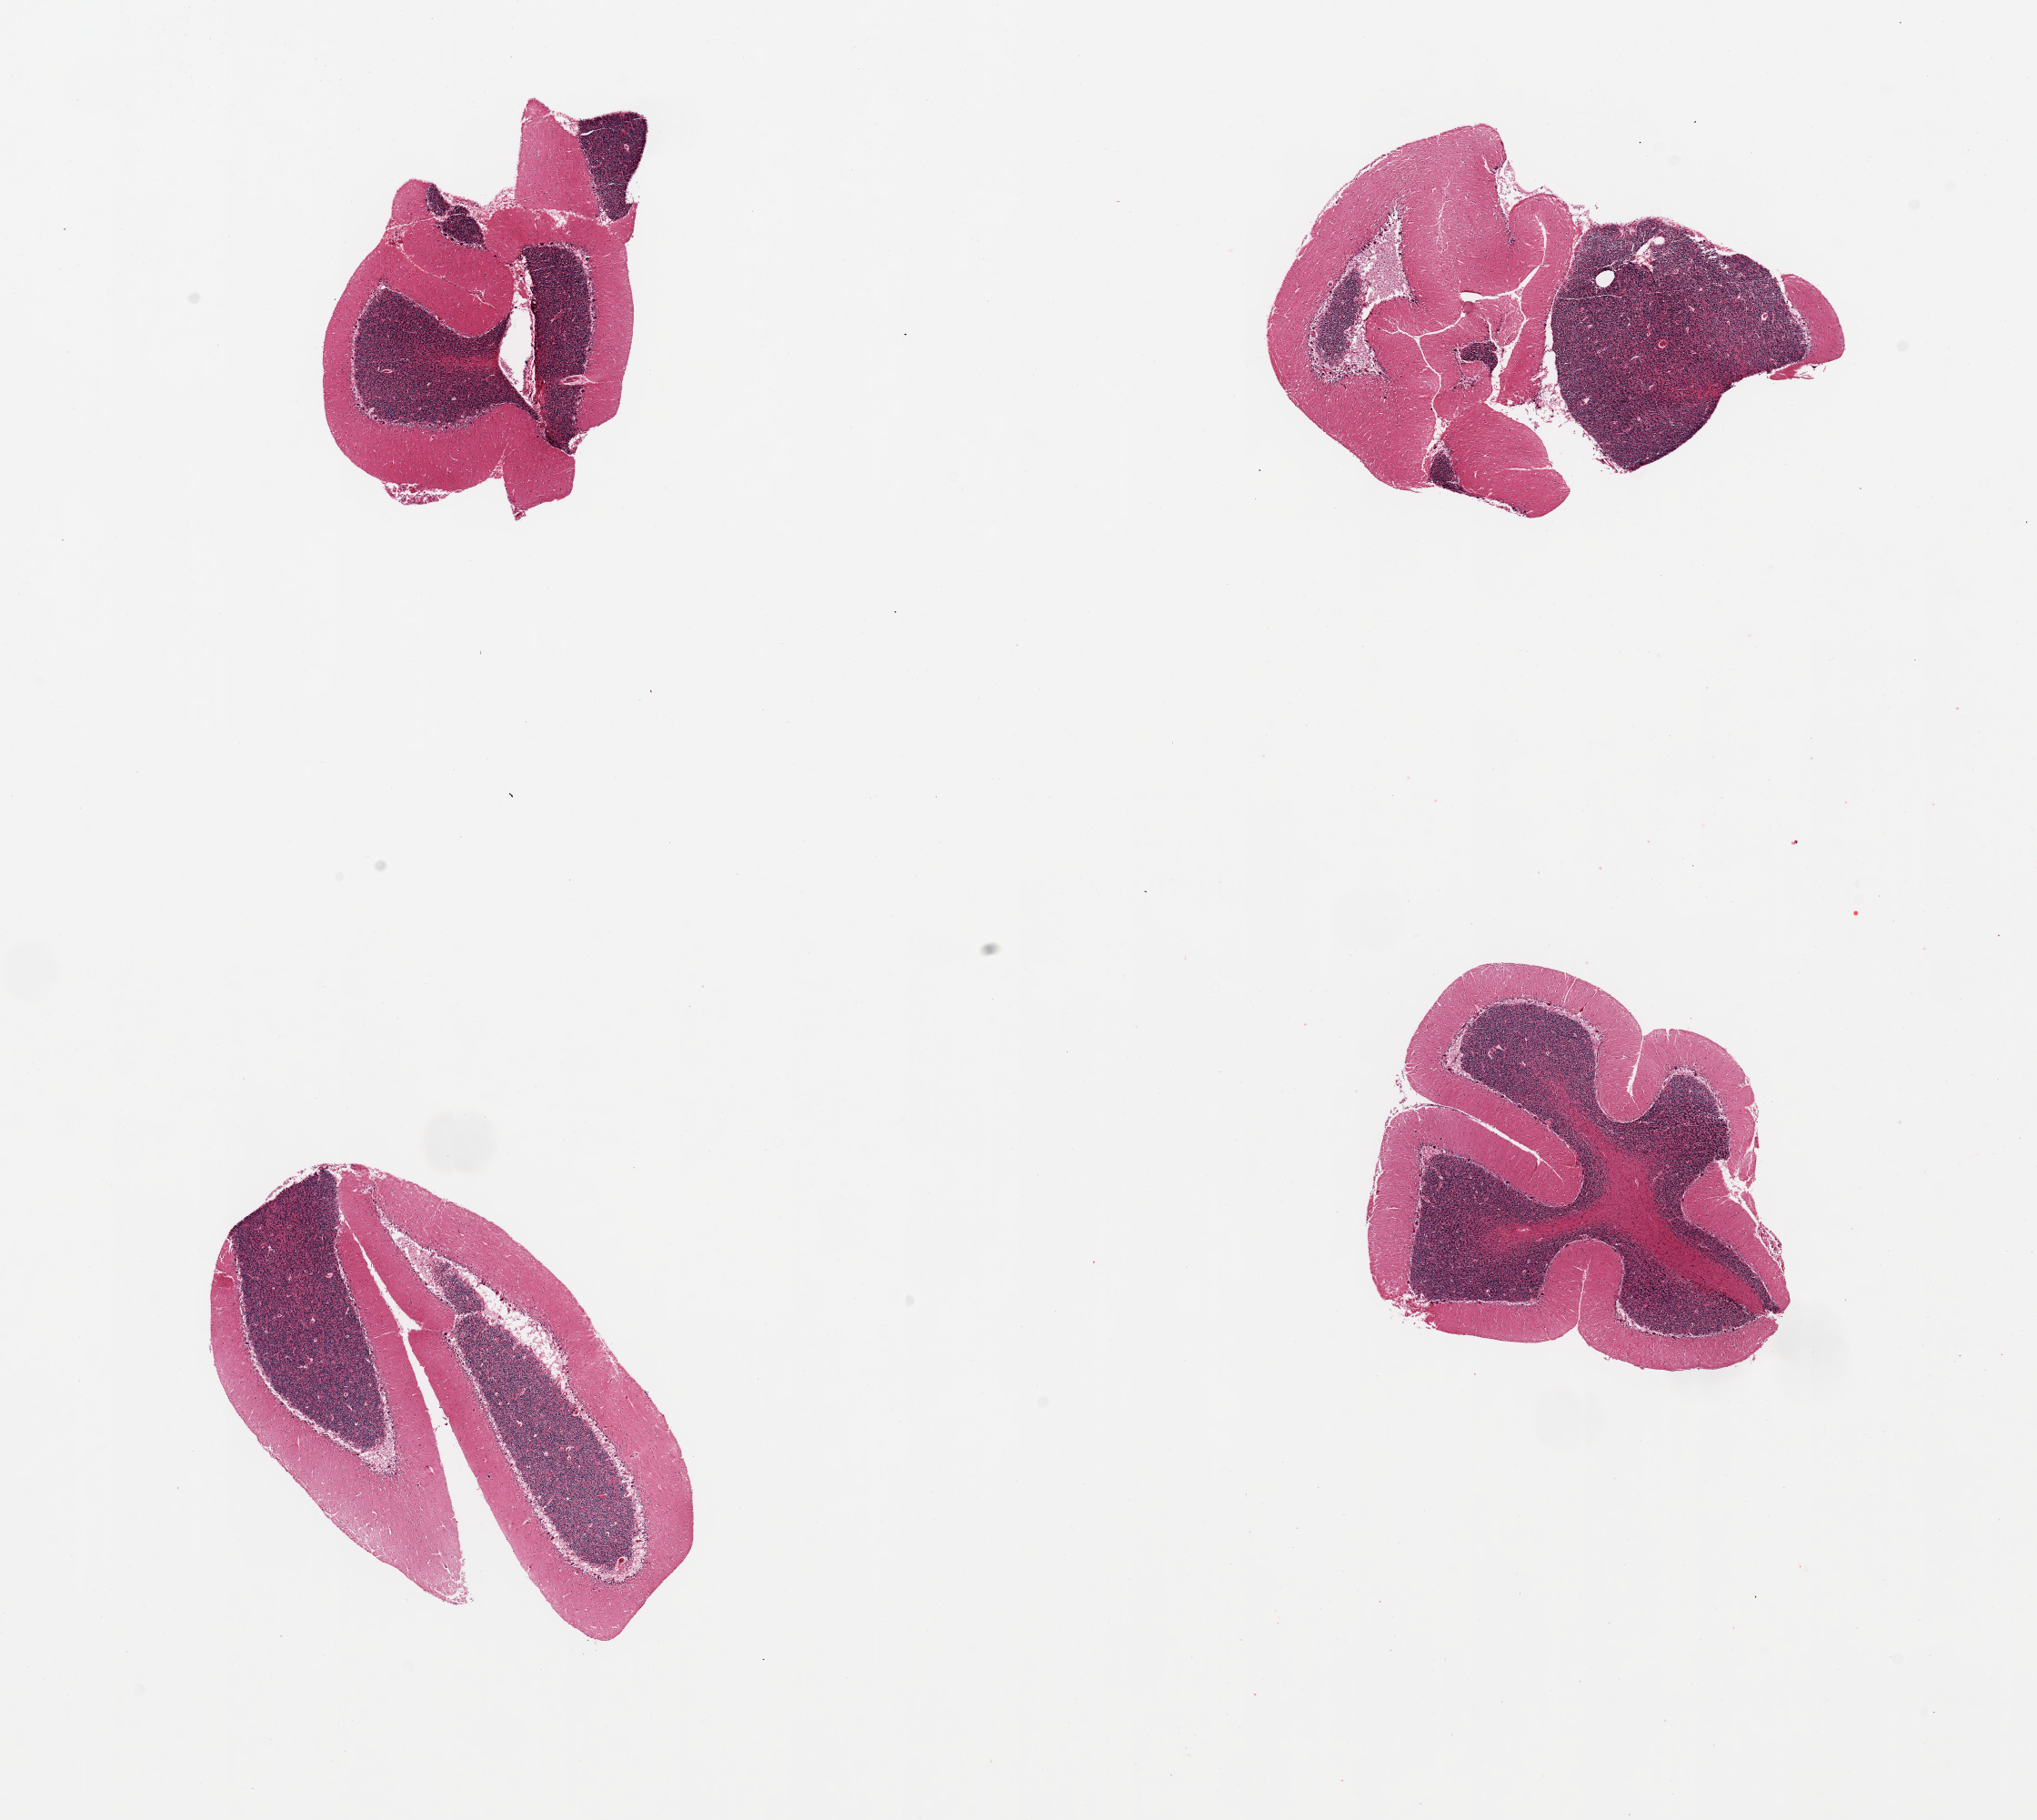
Digitized hematoxylin and eosin (H&E)-stained section — a low-resolution overview of the entire scanned area, about 17.7 x 15.8 mm (from a 20x scan); PAXgene-fixed paraffin-embedded (PFPE) section; target tissue: cerebellum; donor tissue sample. Donor: male.
• review note (as recorded): 4 pieces; Purkinje cells well visualized